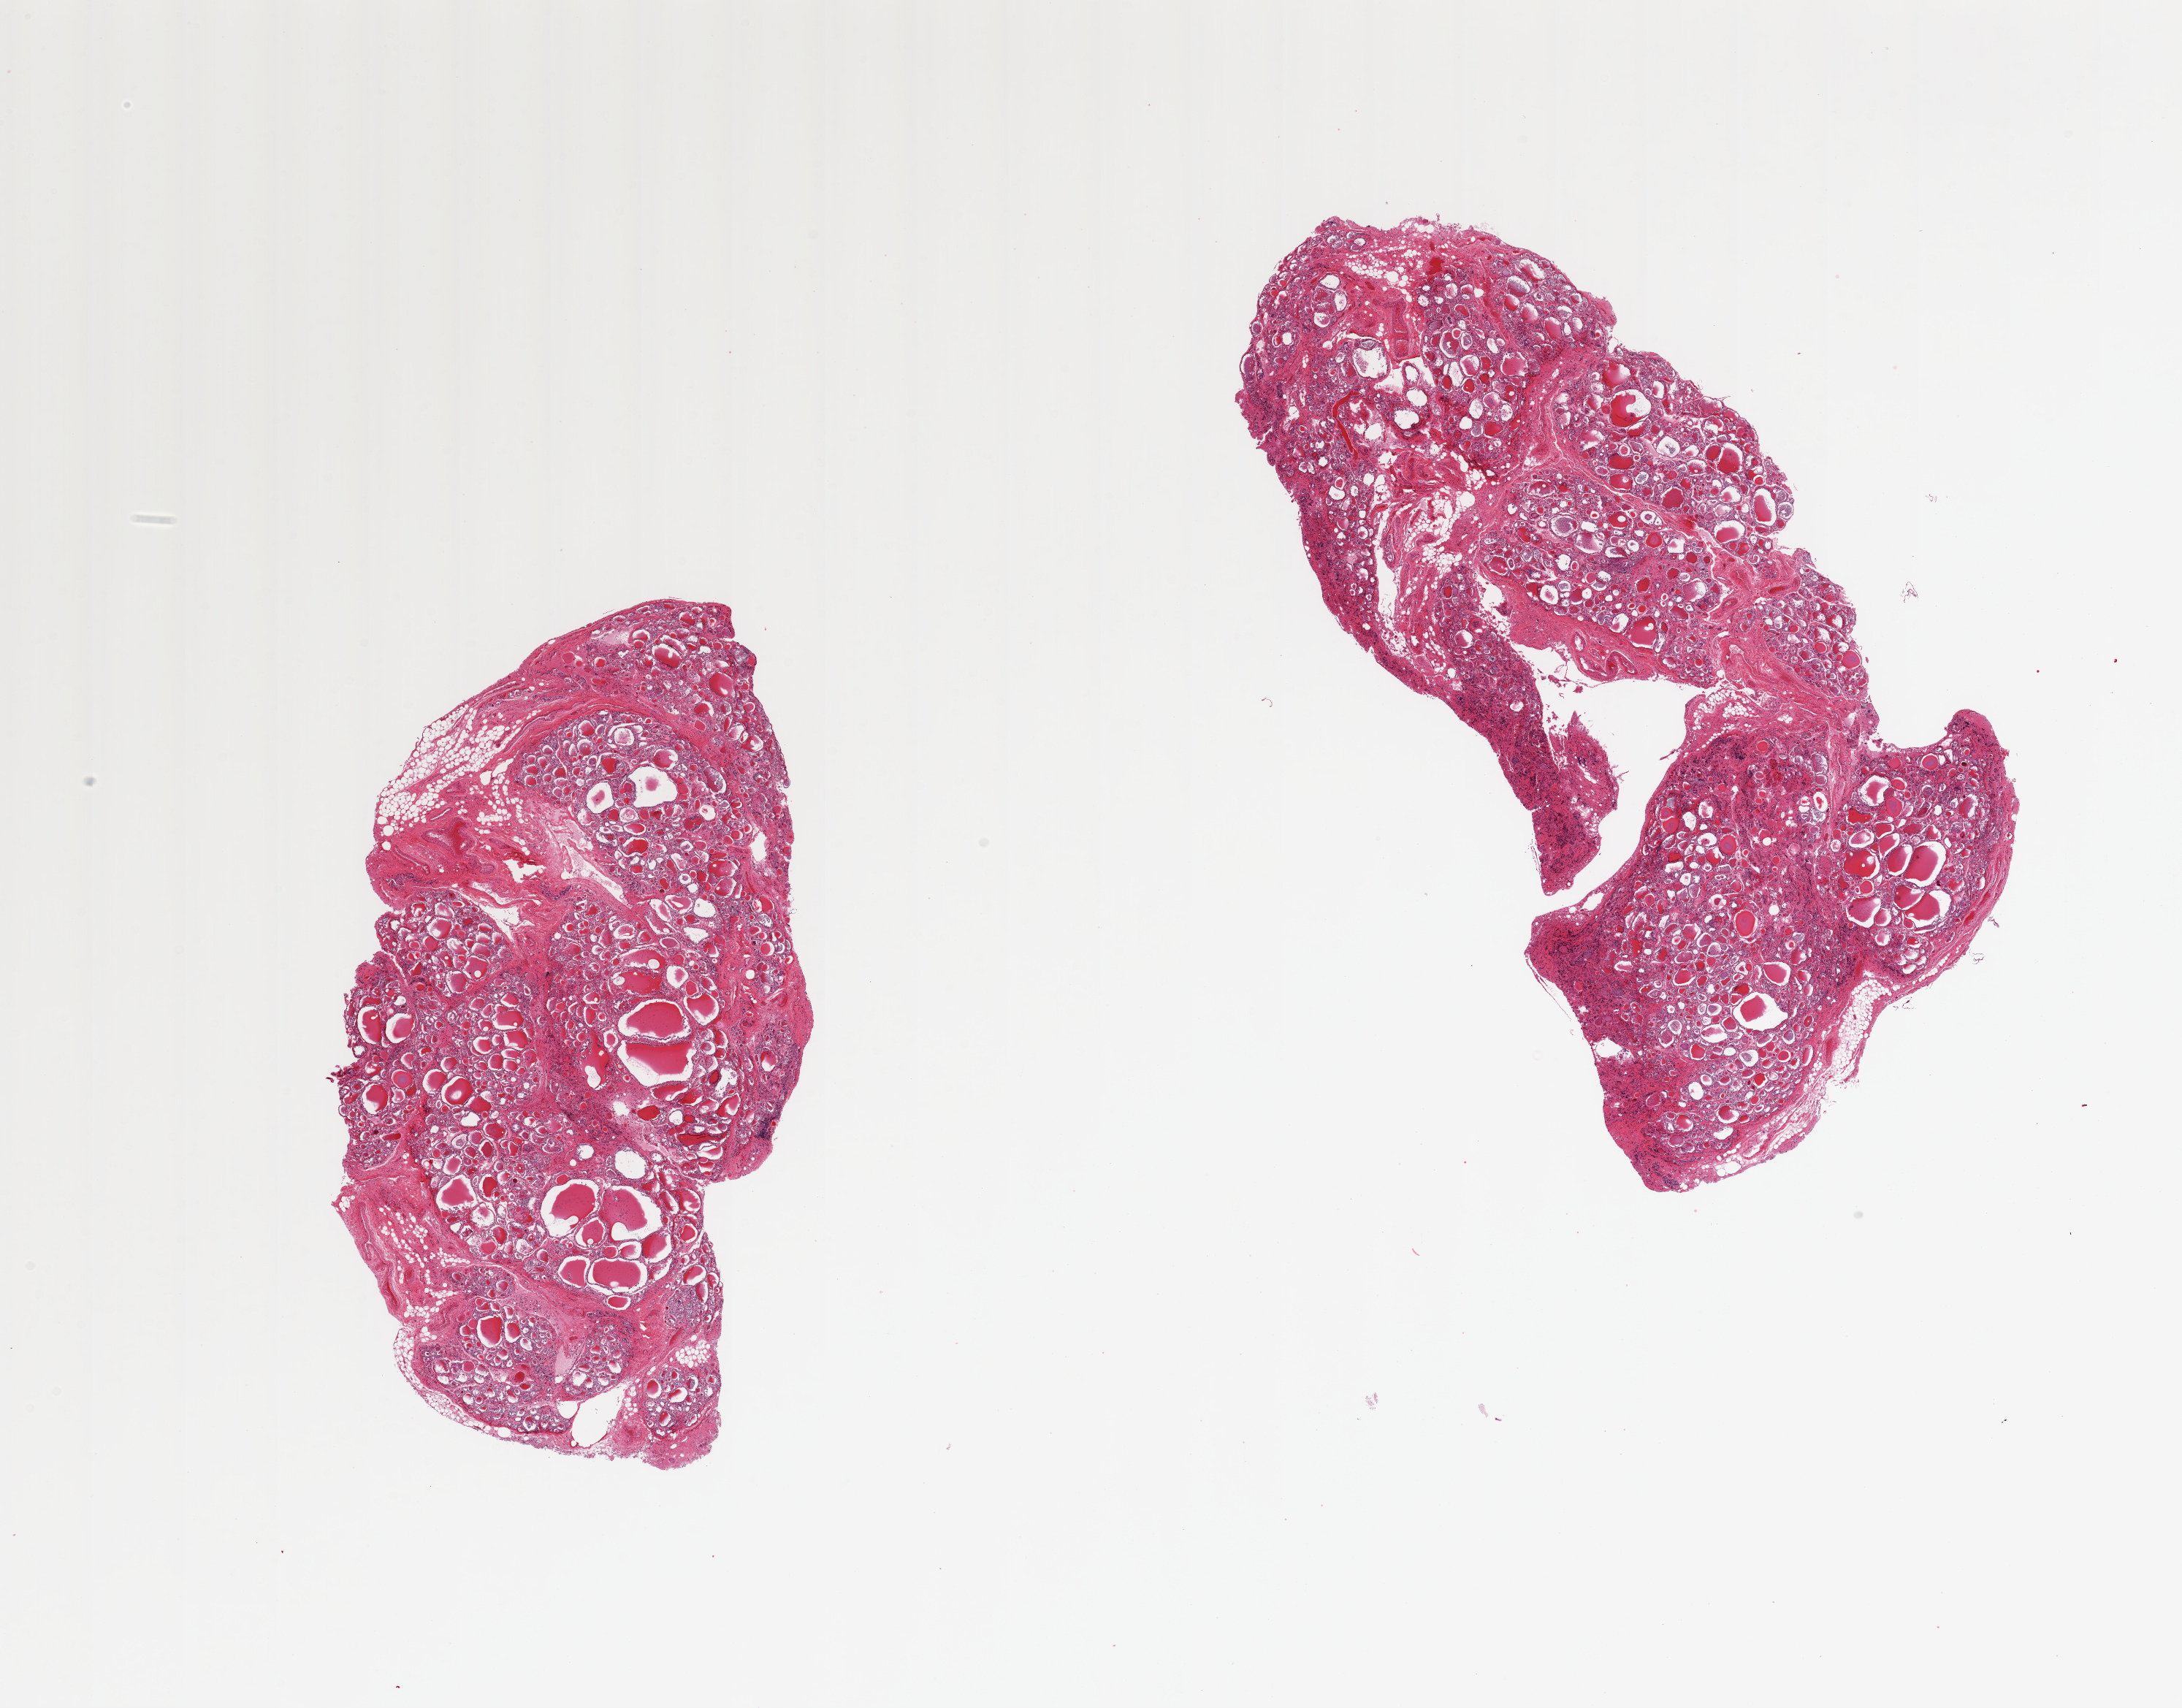
Digitized hematoxylin and eosin (H&E)-stained section — shown as a low-resolution overview of the whole scanned area (about 23.6 x 18.5 mm, acquisition: 20x scan); PAXgene-fixed paraffin-embedded (PFPE) section; sampled site (target tissue): thyroid; donor tissue sample. Male donor.
Pathologist's review note for this sample: 2 pieces, multinodular goitre; regressive changes.